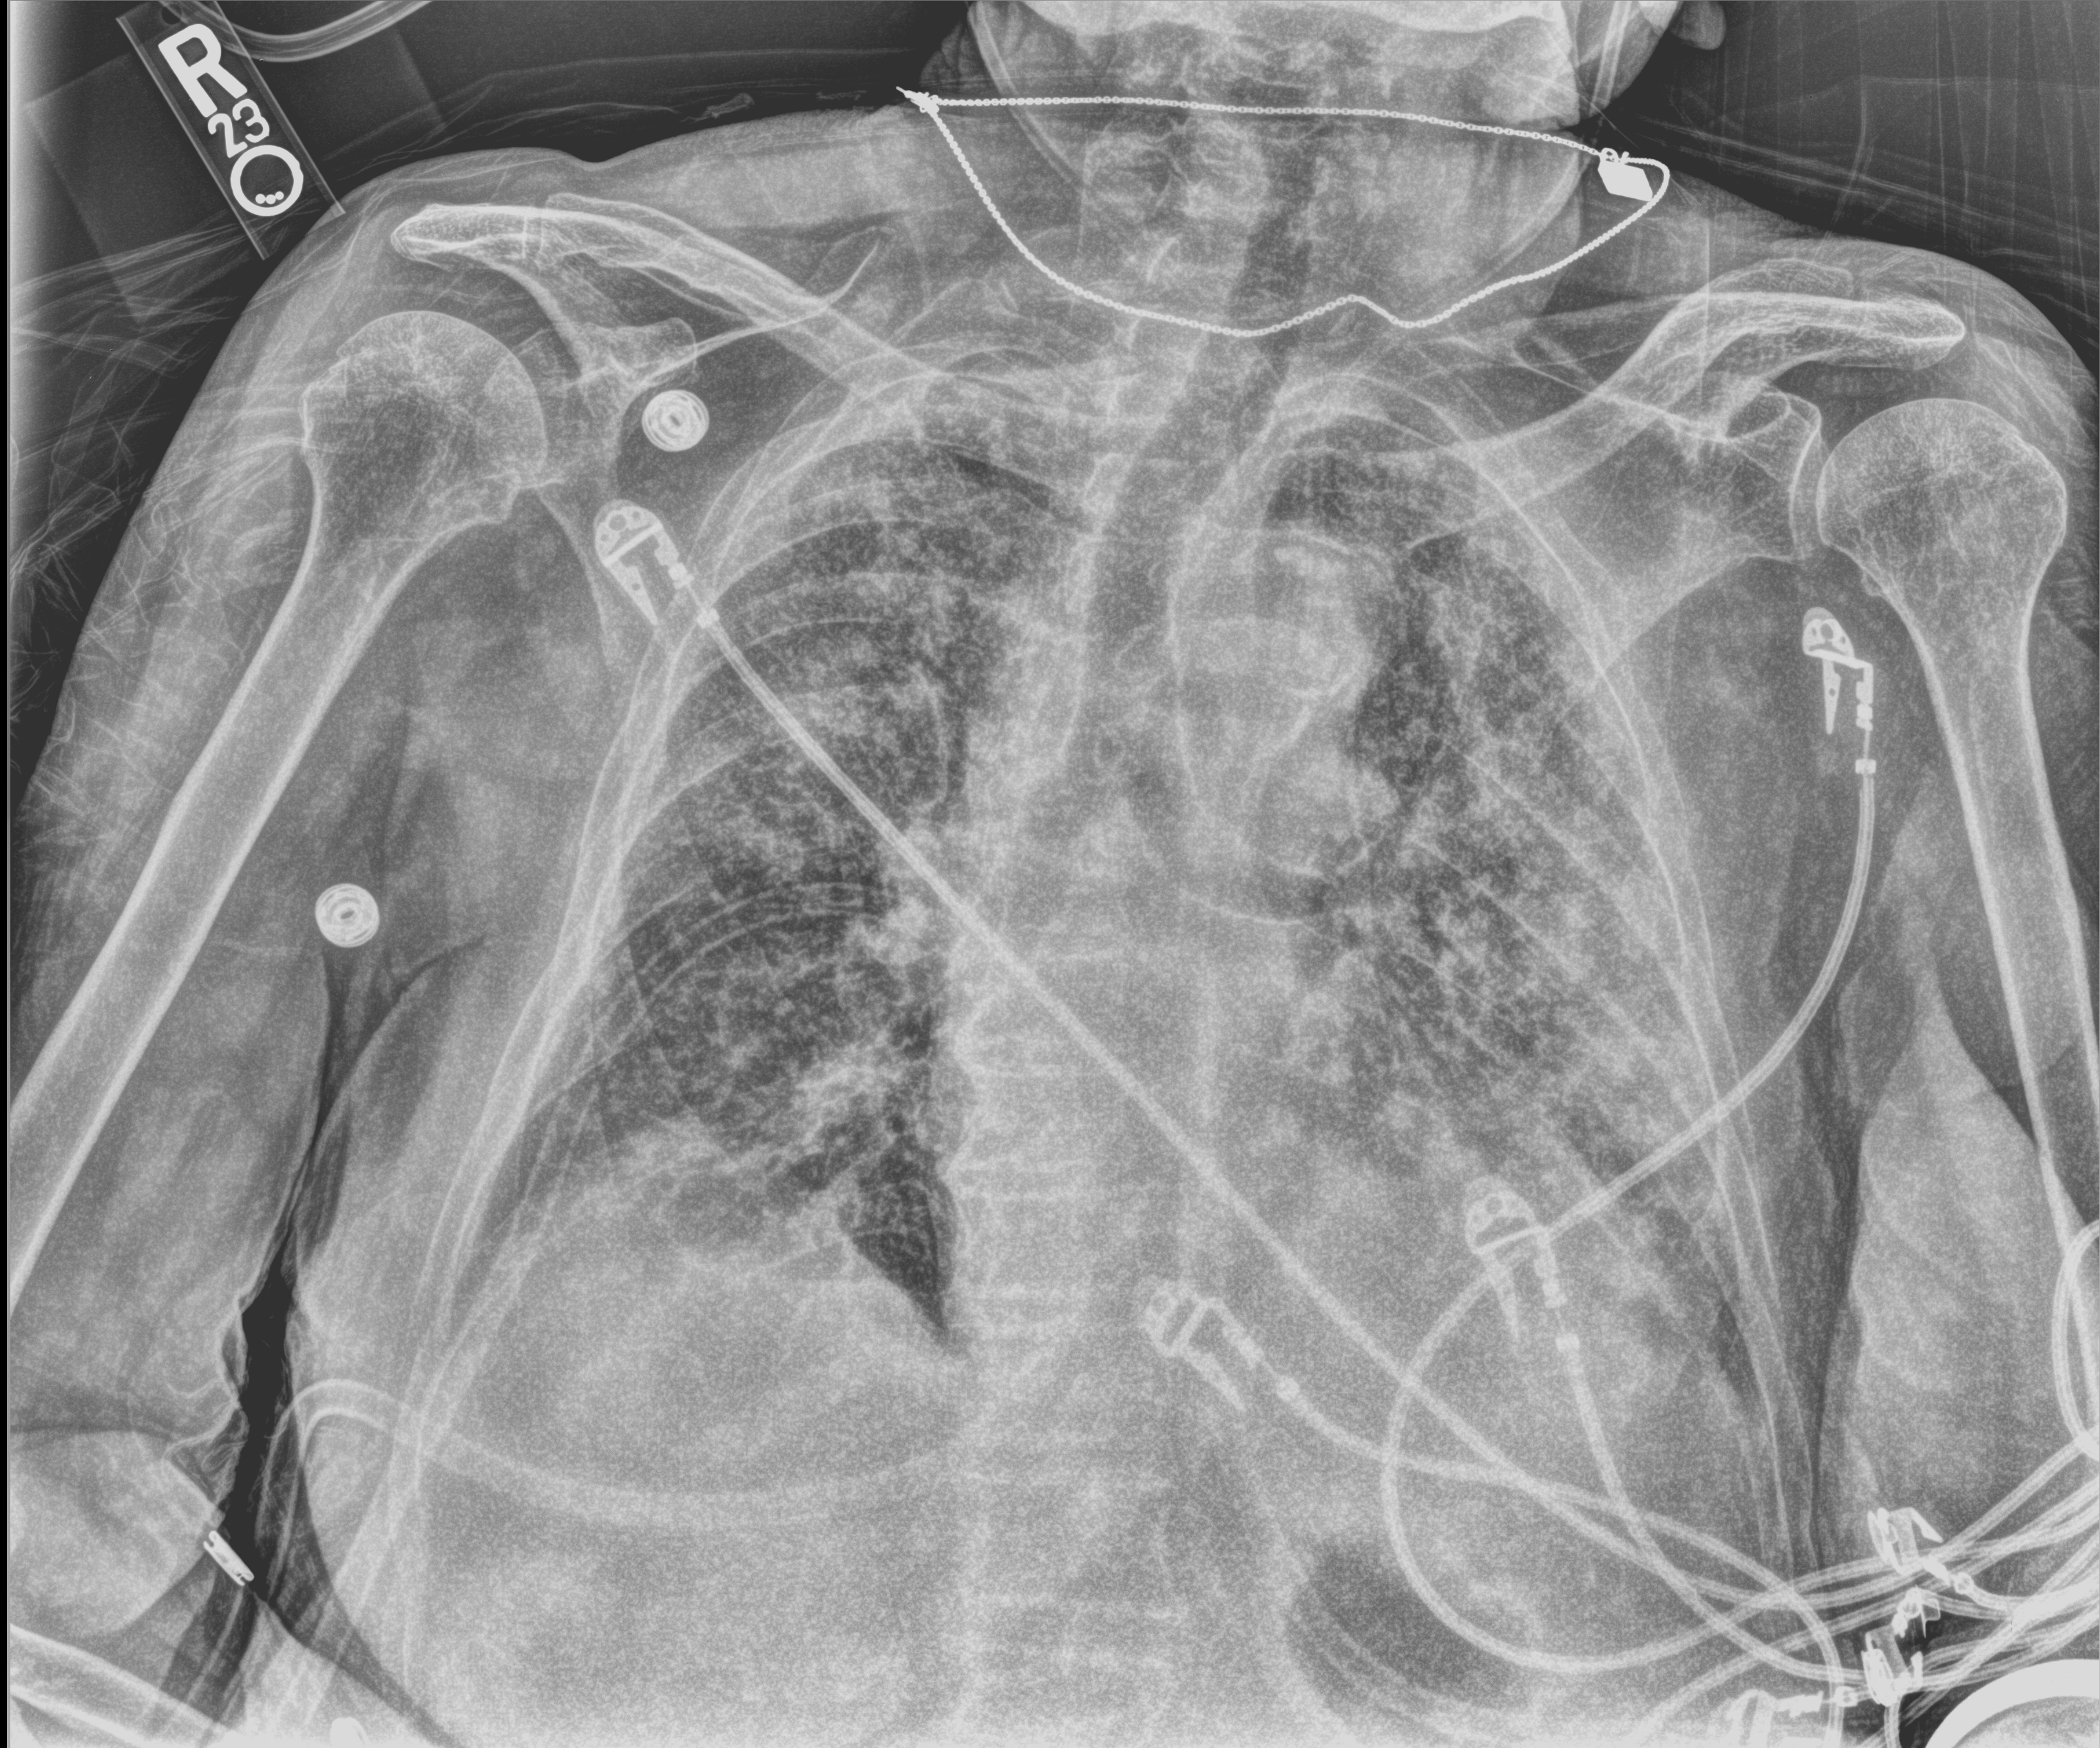
Portable chest radiograph, anteroposterior (AP) projection. Female patient hospitalised with COVID-19, age 75–90 years.
Hospital-stay facts (about this admission, not read from this image; timing relative to this image not recorded): smoking status (admission record): former; length of hospital stay: 13 days; mechanically ventilated during this hospital stay: no.